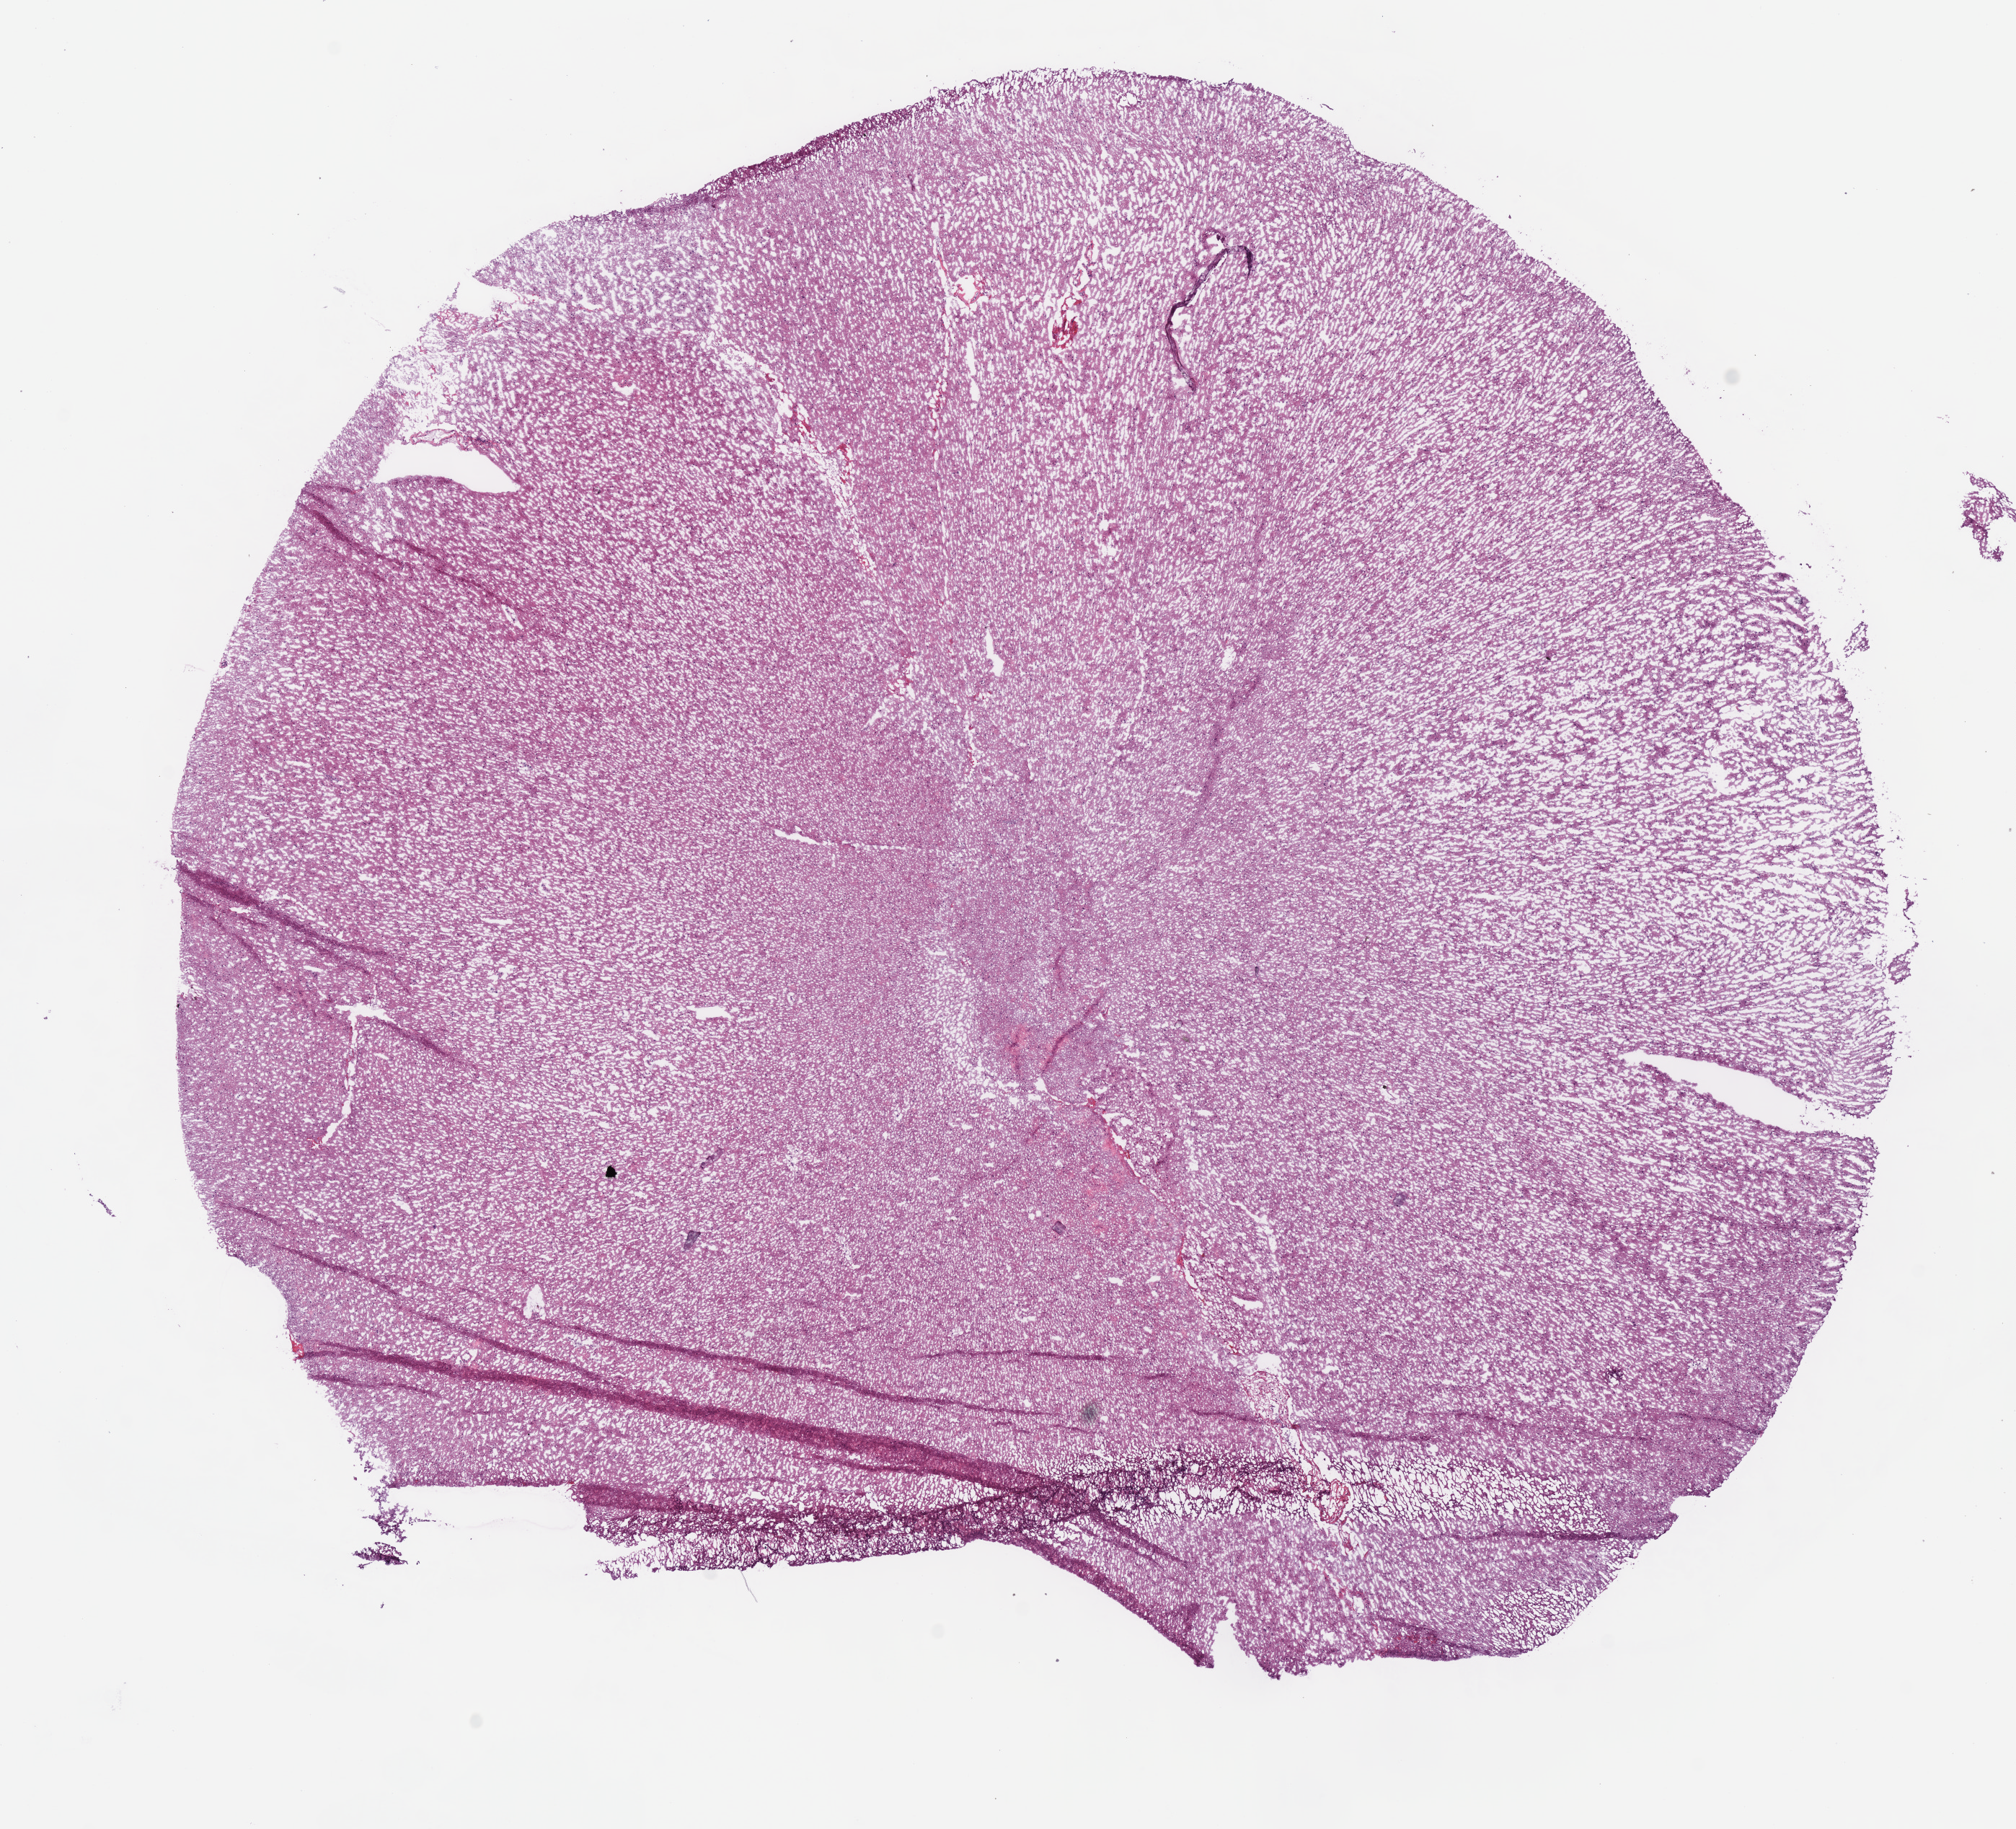
Hematoxylin and eosin (H&E) stained whole-slide image, low-resolution overview of the scanned area, about 11.0 x 10.0 mm (acquisition: 40x scan), frozen section, primary tumour sample from the brain. Male patient; age at initial diagnosis 21 years. Histologic grade: G2 (moderately differentiated). Slide review estimates, as recorded: tumour cells 100%, tumour nuclei 60%, normal cells 0%, stromal cells 0%, necrosis 0%.
* pathologic diagnosis: Oligodendroglioma, NOS
* laterality: right